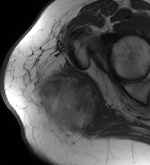
MRI of an extremity soft-tissue mass, one axial slice; MR volume resampled by the dataset authors to the PET/CT grid (not the native acquisition matrix); 150 × 165 image matrix. Female patient. Case-level facts recorded for this patient, not image findings: histological type: epithelioid sarcoma with vascular differentiation; site of the primary tumour: right buttock.
Outlined on this slice (expert contour drawn on MRI and transferred to this co-registered scan by the dataset authors):
- gross tumour volume (mass): box from (x=34, y=74) to (x=99, y=125) px